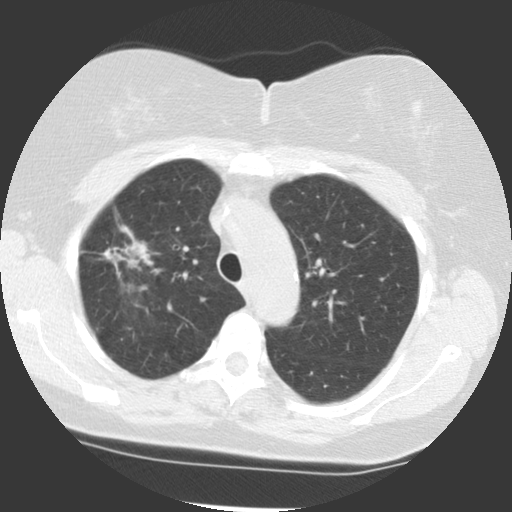
Low-dose screening chest CT, axial slice, baseline screening round, lung window (W 1500 / L -600 HU), standard (soft-tissue) reconstruction kernel (STANDARD), slice 87 of 113 in the series. Female, age 68 years at enrolment. Former smoker at enrolment.
Expert reader's lesion annotation, box from (x=87, y=231) to (x=155, y=290) px. The exam's reader record, not a measurement of the box and not confirmed to be the same lesion: non-calcified nodule or mass ≥4 mm, right upper lobe, 42 × 20 mm, spiculated (stellate) margins, soft tissue attenuation. Official screen result: positive, change unspecified: nodule(s) >= 4 mm or enlarging nodule(s), mass(es), or other non-specific abnormalities suspicious for lung cancer. Participant outcome: lung cancer diagnosed 51 days after this screen — adenocarcinoma, NOS, right upper lobe, moderately differentiated (G2), stage IB (AJCC 6th edition), 31 mm at pathology.